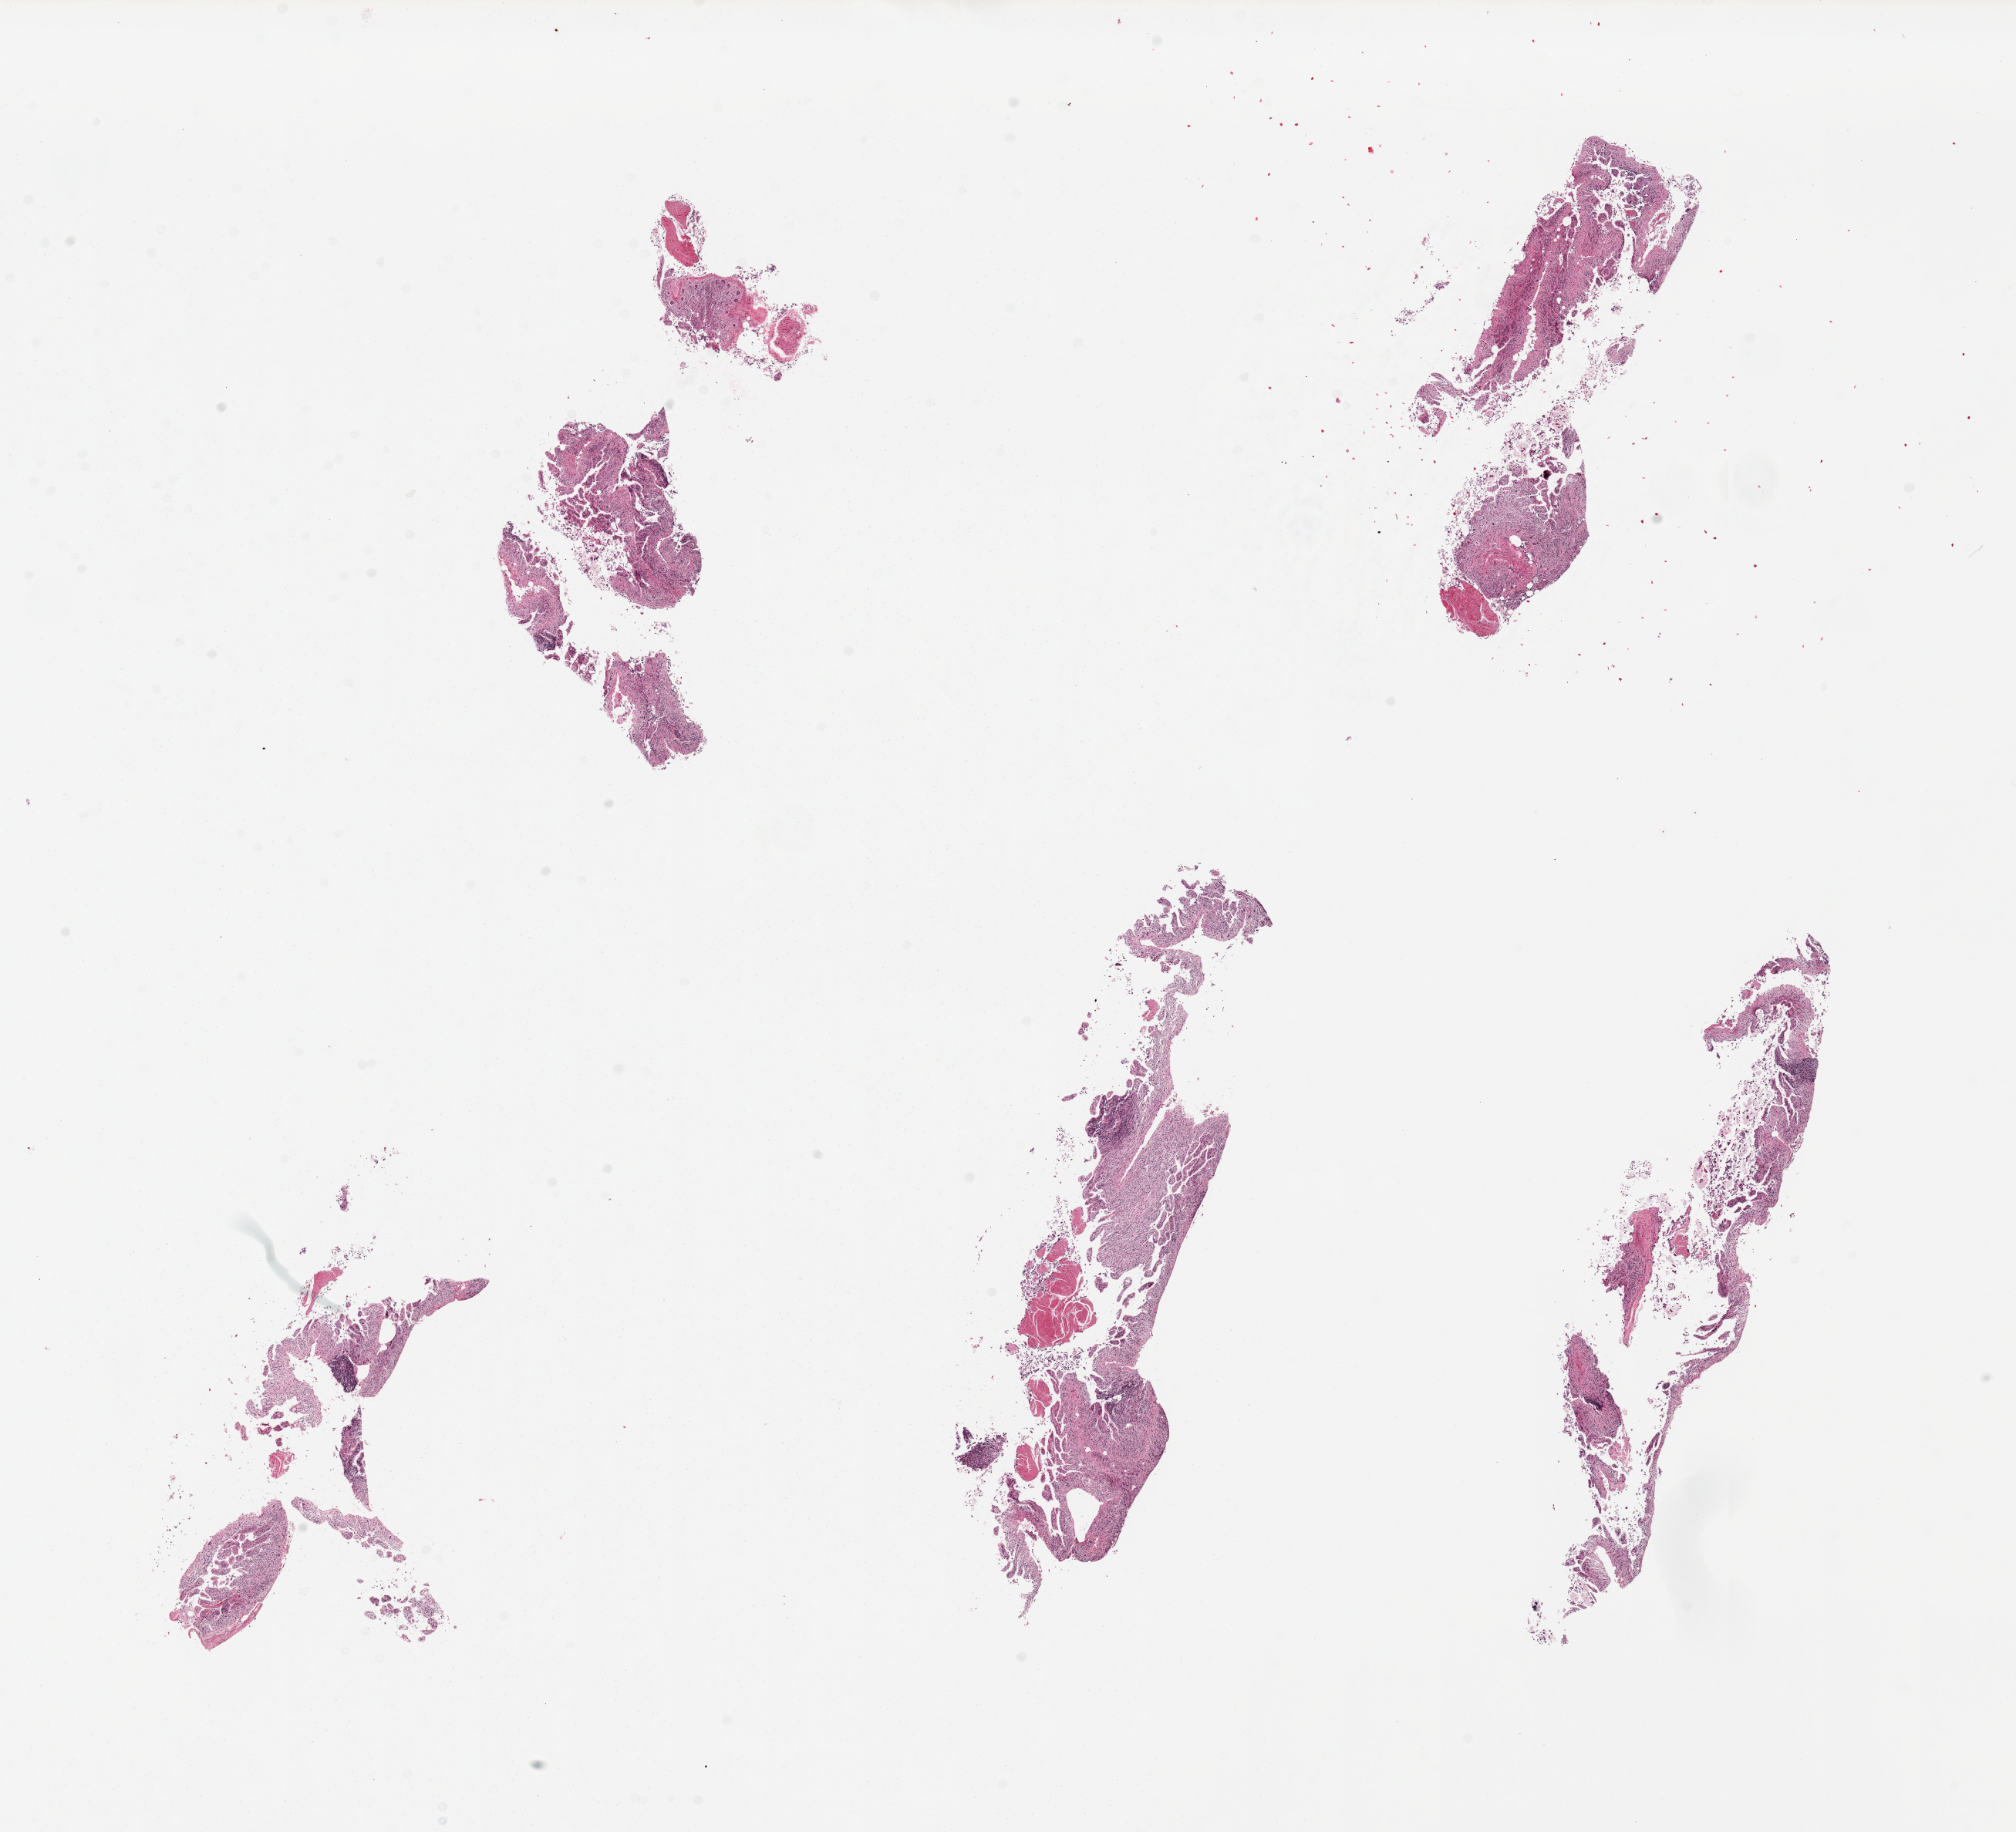
Whole-slide image, hematoxylin and eosin (H&E) stain, brightfield — shown as a low-resolution overview of the whole scanned area (about 20.7 x 18.8 mm, acquisition: 20x scan), PAXgene-fixed, paraffin-embedded tissue, target tissue: ileum, donor tissue sample.
Pathologist's review note for this sample: 5 pieces, up to 7x2mm allautolyzed mucosa; lymphoid follicles ~5-10% of total.